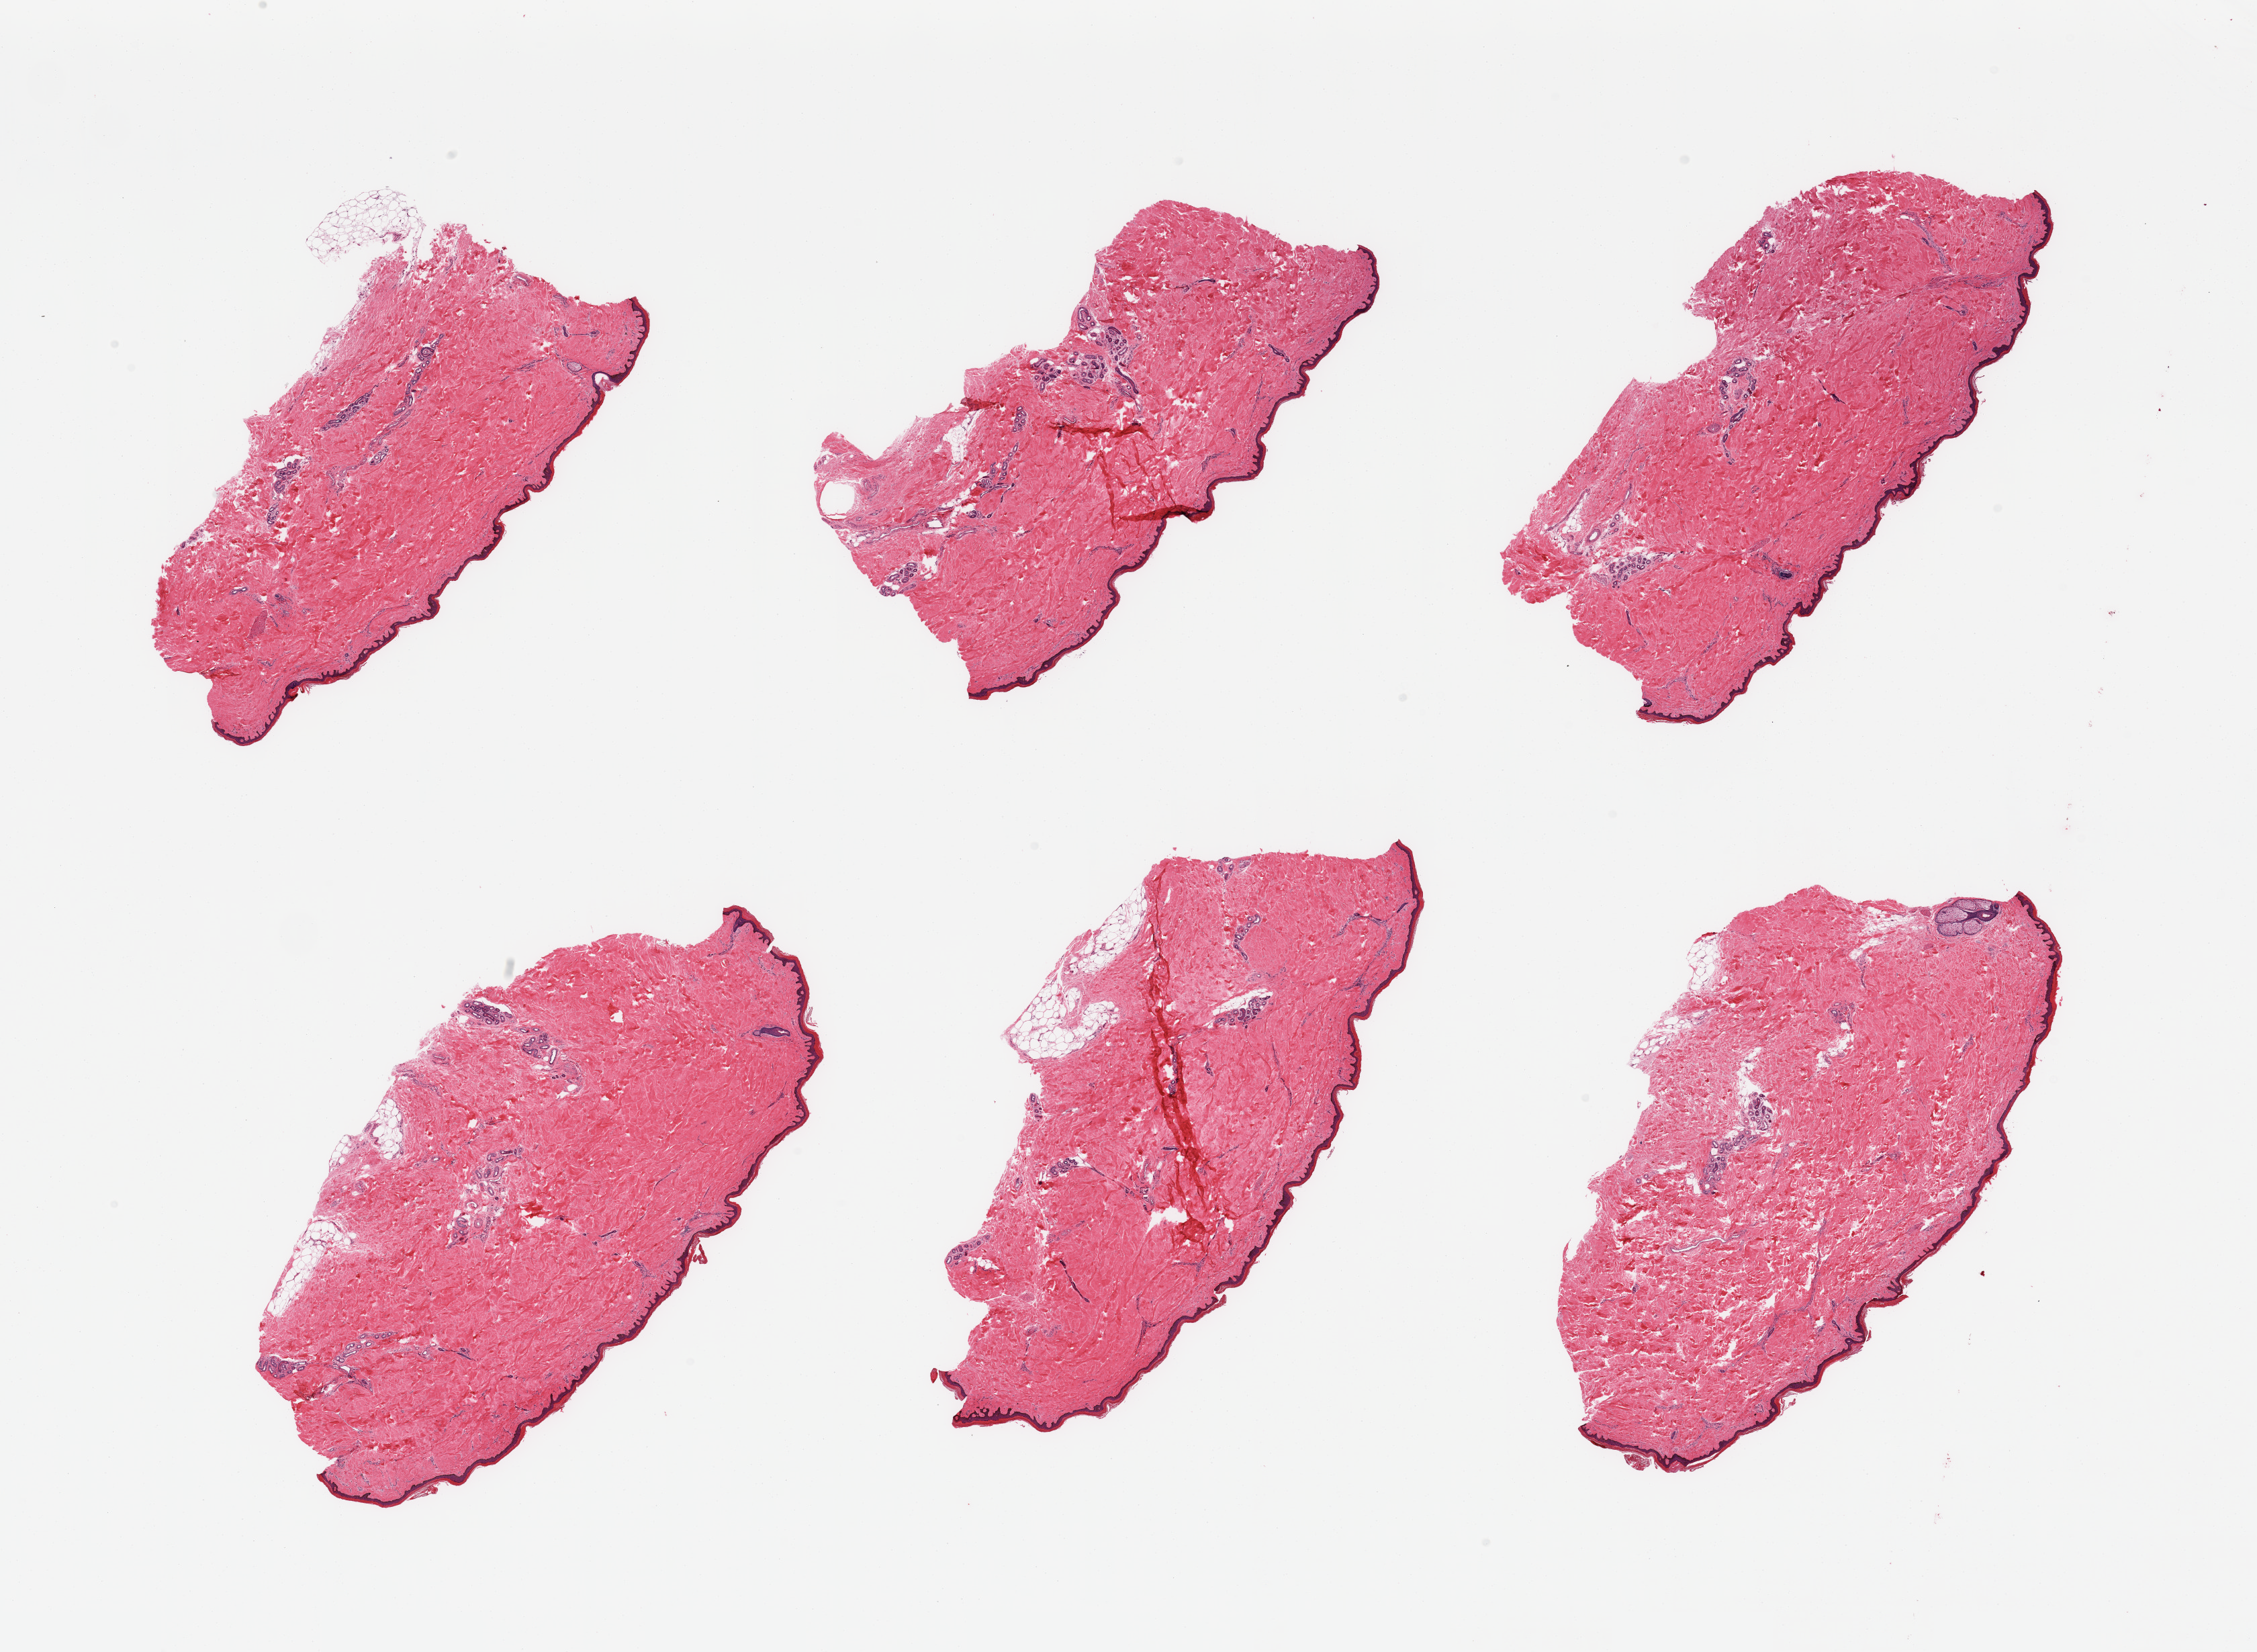
Digitized hematoxylin and eosin (H&E)-stained section, brightfield, low-resolution overview of the scanned area, about 26.6 x 19.5 mm (slide scanned at 20x), PAXgene-fixed paraffin-embedded (PFPE) section, target tissue: skin of lower leg, donor tissue sample. Male donor.
Review note (as recorded): 6 pieces; well trimmed; <5% dermal fat; 36um thick epidermis.